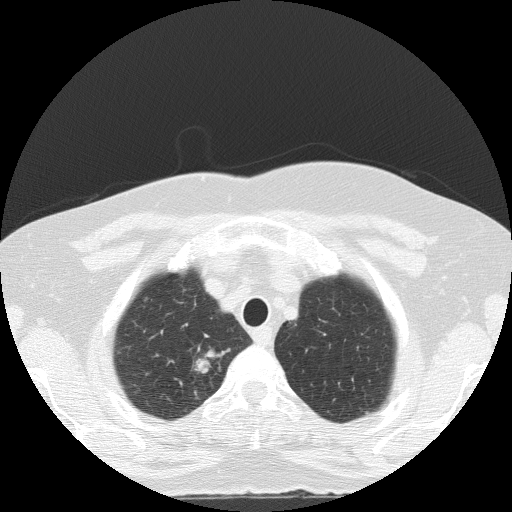
Low-dose screening chest CT, axial slice. Baseline annual screen. Lung window (W 1500 / L -600 HU). 2 mm slice thickness. Lung (sharp) reconstruction kernel (FC51). 120 kVp. 512 × 512 image matrix, field of view 320 × 320 mm. Female participant, aged 56 years at enrolment.
- Lesion marked by an expert reader, bounding box <174,344,230,388> (left, top, right, bottom; pixels).
- The screening reader recorded 2 non-calcified nodules or masses ≥4 mm on this exam (right upper lobe, right lower lobe); which of them this box marks is not recorded.
- Lung cancer was diagnosed 24 days after this screen: adenocarcinoma, NOS, right upper lobe, poorly differentiated (G3), stage IA (AJCC 6th edition), 20 mm at pathology.